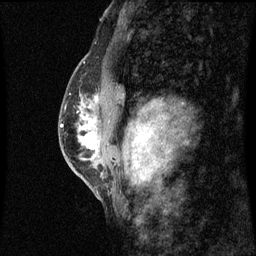
Breast MRI (dynamic contrast-enhanced), one sagittal slice. Slice 37 of 60 in the series (ordered by position). Dynamic contrast-enhanced series, image 2 of 3 at this slice position (ordered by acquisition). 1.5 T. TE 4.2 ms, TR 8.9 ms. 2 mm slice thickness. 256 × 256 image matrix, field of view 200 × 200 mm. Female patient, age 50 years. Case-level facts recorded for this patient, not image findings: setting: breast cancer imaged before/during neoadjuvant chemotherapy; receptor status: triple-negative.
Structures marked on this image (semi-automatically segmented with operator editing):
- analysis volume of interest (the breast-tissue region the enhancement analysis was run in; not a lesion): box from (x=68, y=80) to (x=101, y=169) px
- tumour enhancement mask (voxels above the 70 % enhancement threshold inside the analysis volume of interest): (x=81, y=118)–(x=97, y=149)